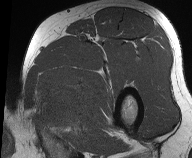
MRI of an extremity soft-tissue mass, one axial slice. Position 43 of 61 along the scan axis. MR volume resampled by the dataset authors to the PET/CT grid (not the native acquisition matrix). 192 × 158 image matrix, field of view 187 × 154 mm. Male patient. Case-level facts recorded for this patient, not image findings: histological type: pleiomorphic liposarcoma; grade: high; site of the primary tumour: left thigh.
Outlined on this slice (expert contour drawn on MRI and transferred to this co-registered scan by the dataset authors):
- gross tumour volume including surrounding oedema: bounding box [x1, y1, x2, y2] px = [32, 73, 90, 131]
- gross tumour volume (mass): [41, 78, 78, 108]